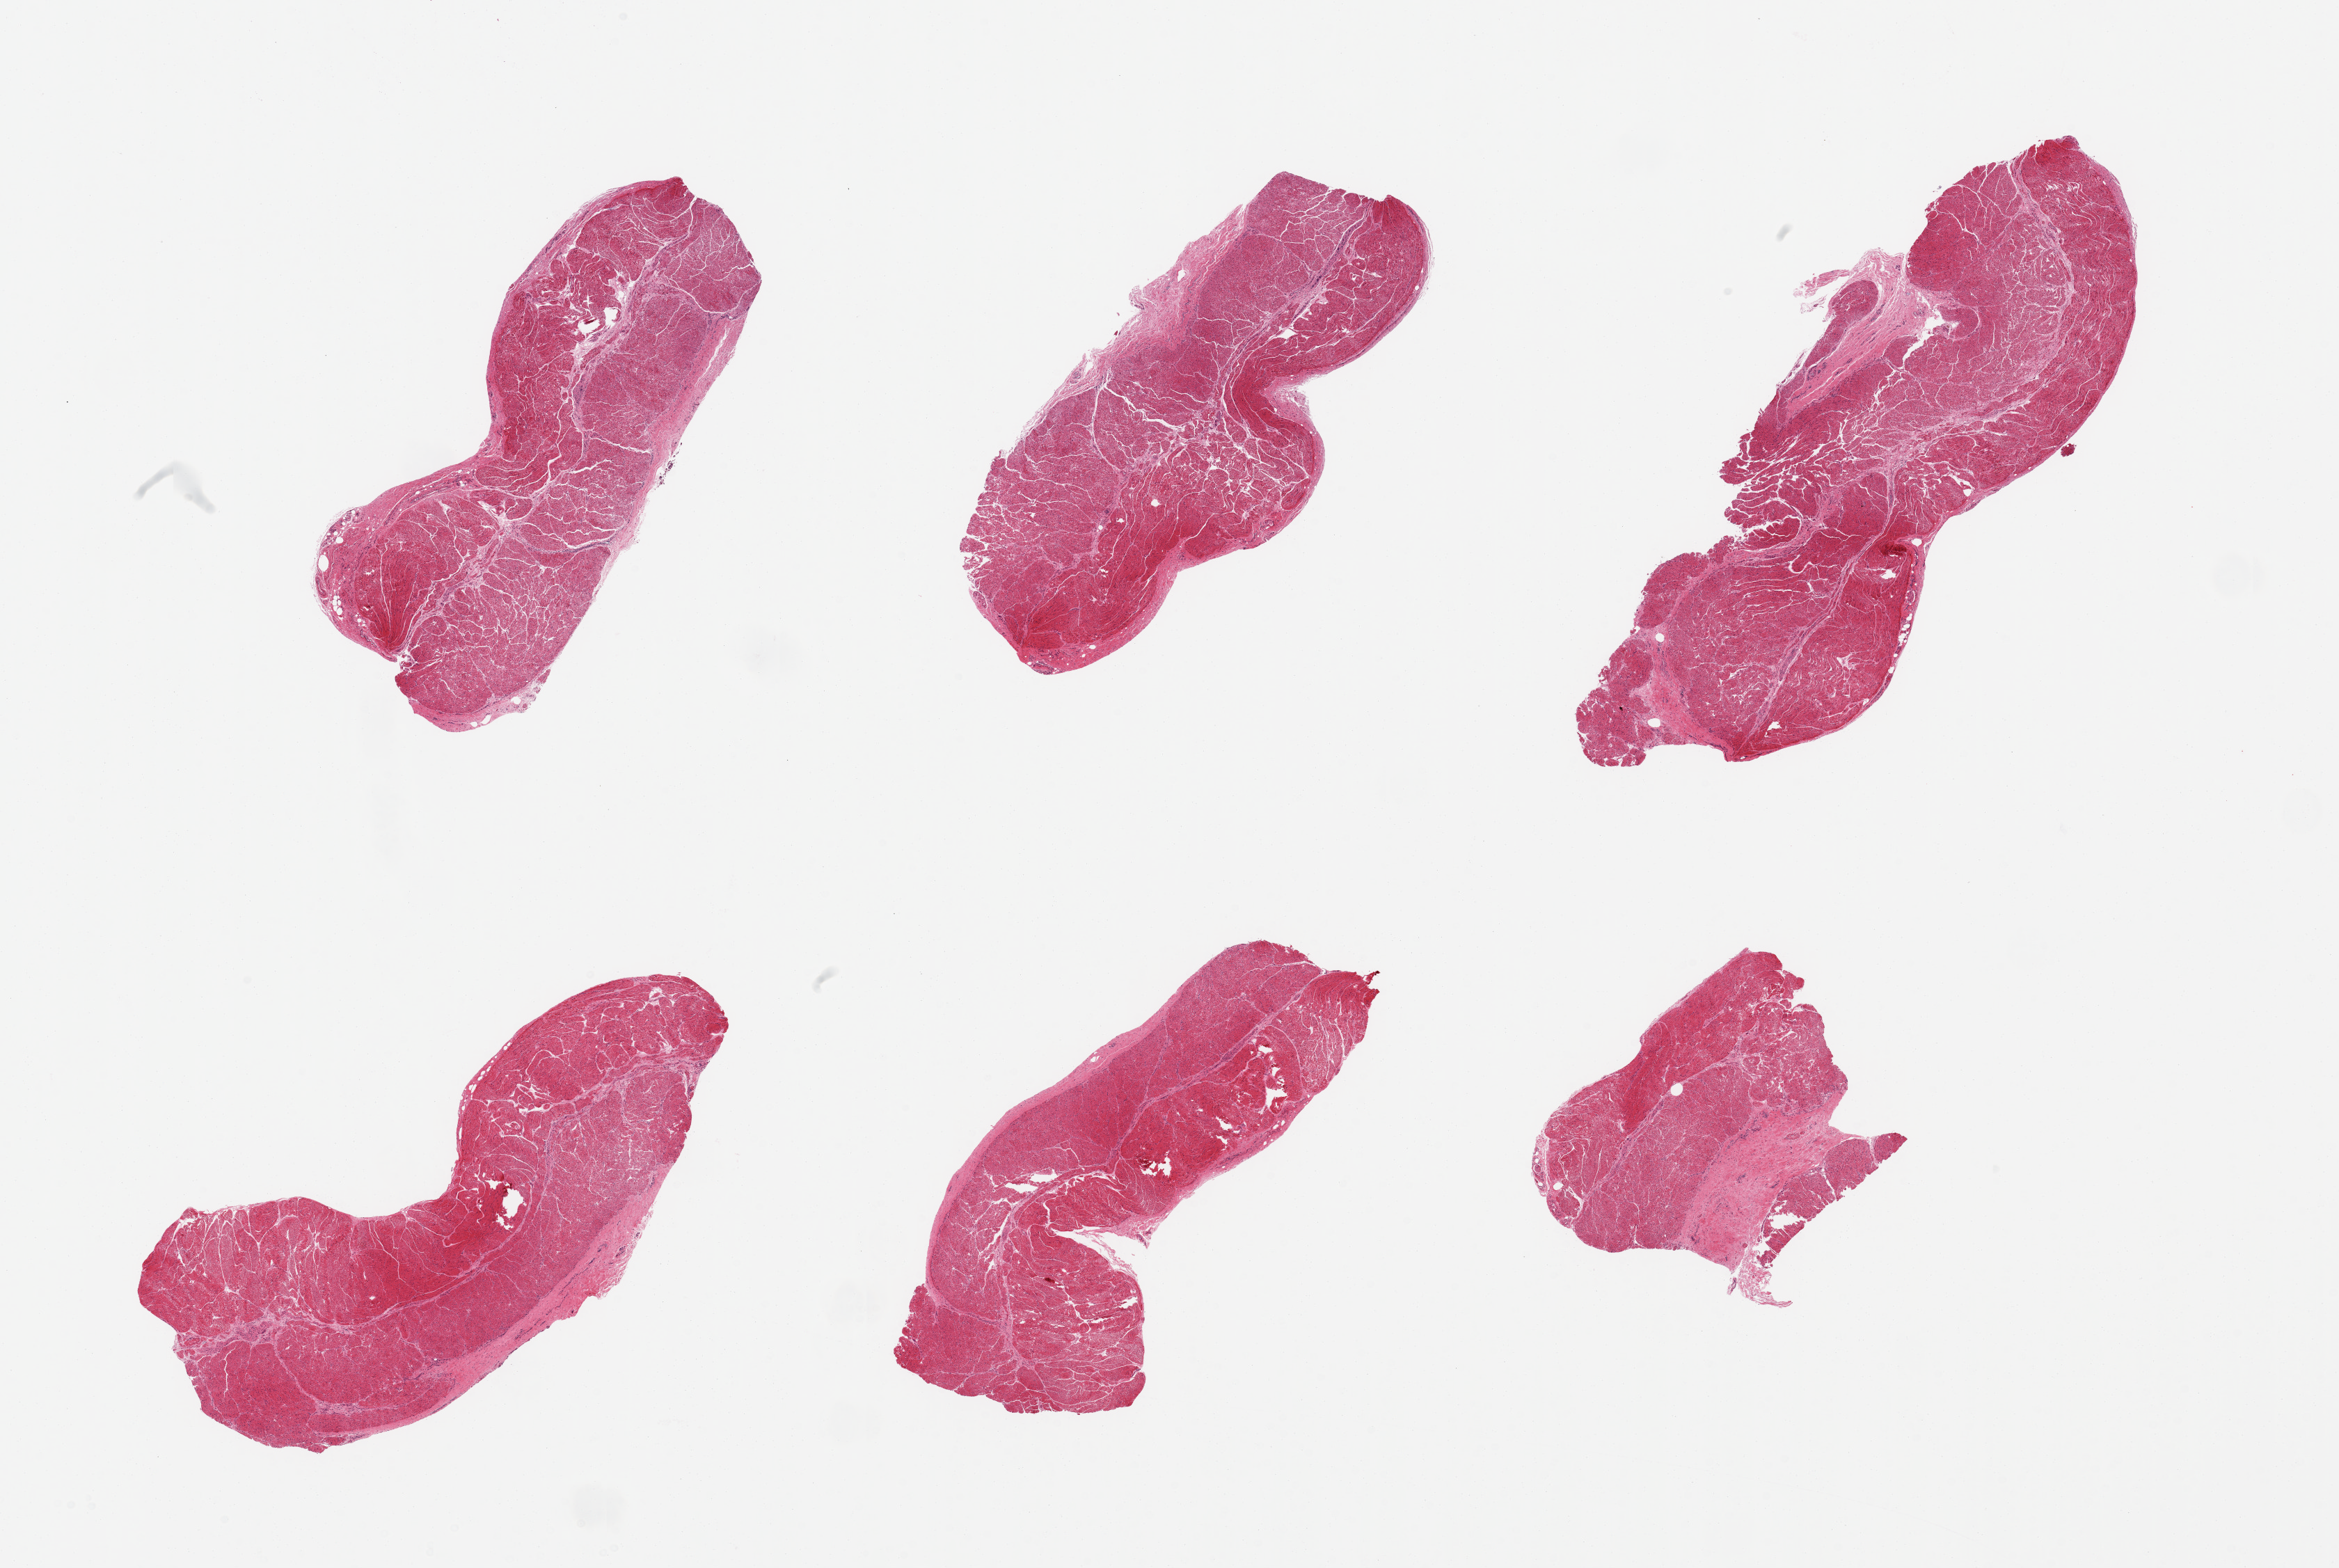
Digitized haematoxylin and eosin-stained section, a low-resolution overview of the entire scanned area, about 26.6 x 17.8 mm; PAXgene-fixed paraffin-embedded (PFPE) section; target tissue: esophageal muscle; tissue donor sample. Male donor.
Review note (as recorded): 6 pieces; muscularis.